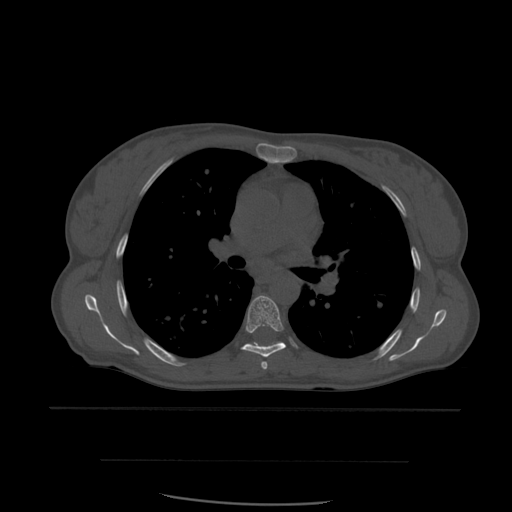
CT including the spine, one axial slice; bone window (W 1800 / L 400 HU); 1.25 mm slice thickness; 512 × 512 image matrix. Patient age 48 years. Case-level facts recorded for this patient, not image findings: primary cancer: lung.
Outlined on this slice (semi-automatically segmented with operator editing):
- T5 vertebra: bounding box [x1, y1, x2, y2] px = [261, 361, 268, 370]
- T6 vertebra: [241, 296, 286, 358]
- T7 vertebra: [256, 342, 283, 347]